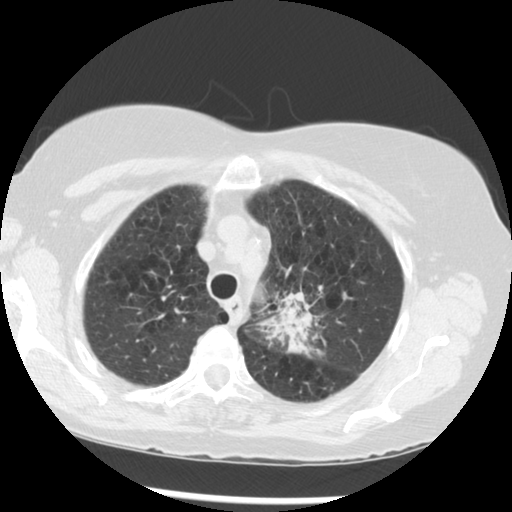
Low-dose screening chest CT, one axial slice. Reconstruction kernel STANDARD. 120 kVp. Lung window (W 1500 / L -600 HU). 2.5 mm slice thickness. 512 × 512 image matrix, field of view 330 × 330 mm.
Annotated regions visible in this slice (outlined manually by an expert reader):
- lesion 1 (tumor, upper lobe of left lung): bounding box <272,292,319,358> (left, top, right, bottom; pixels)